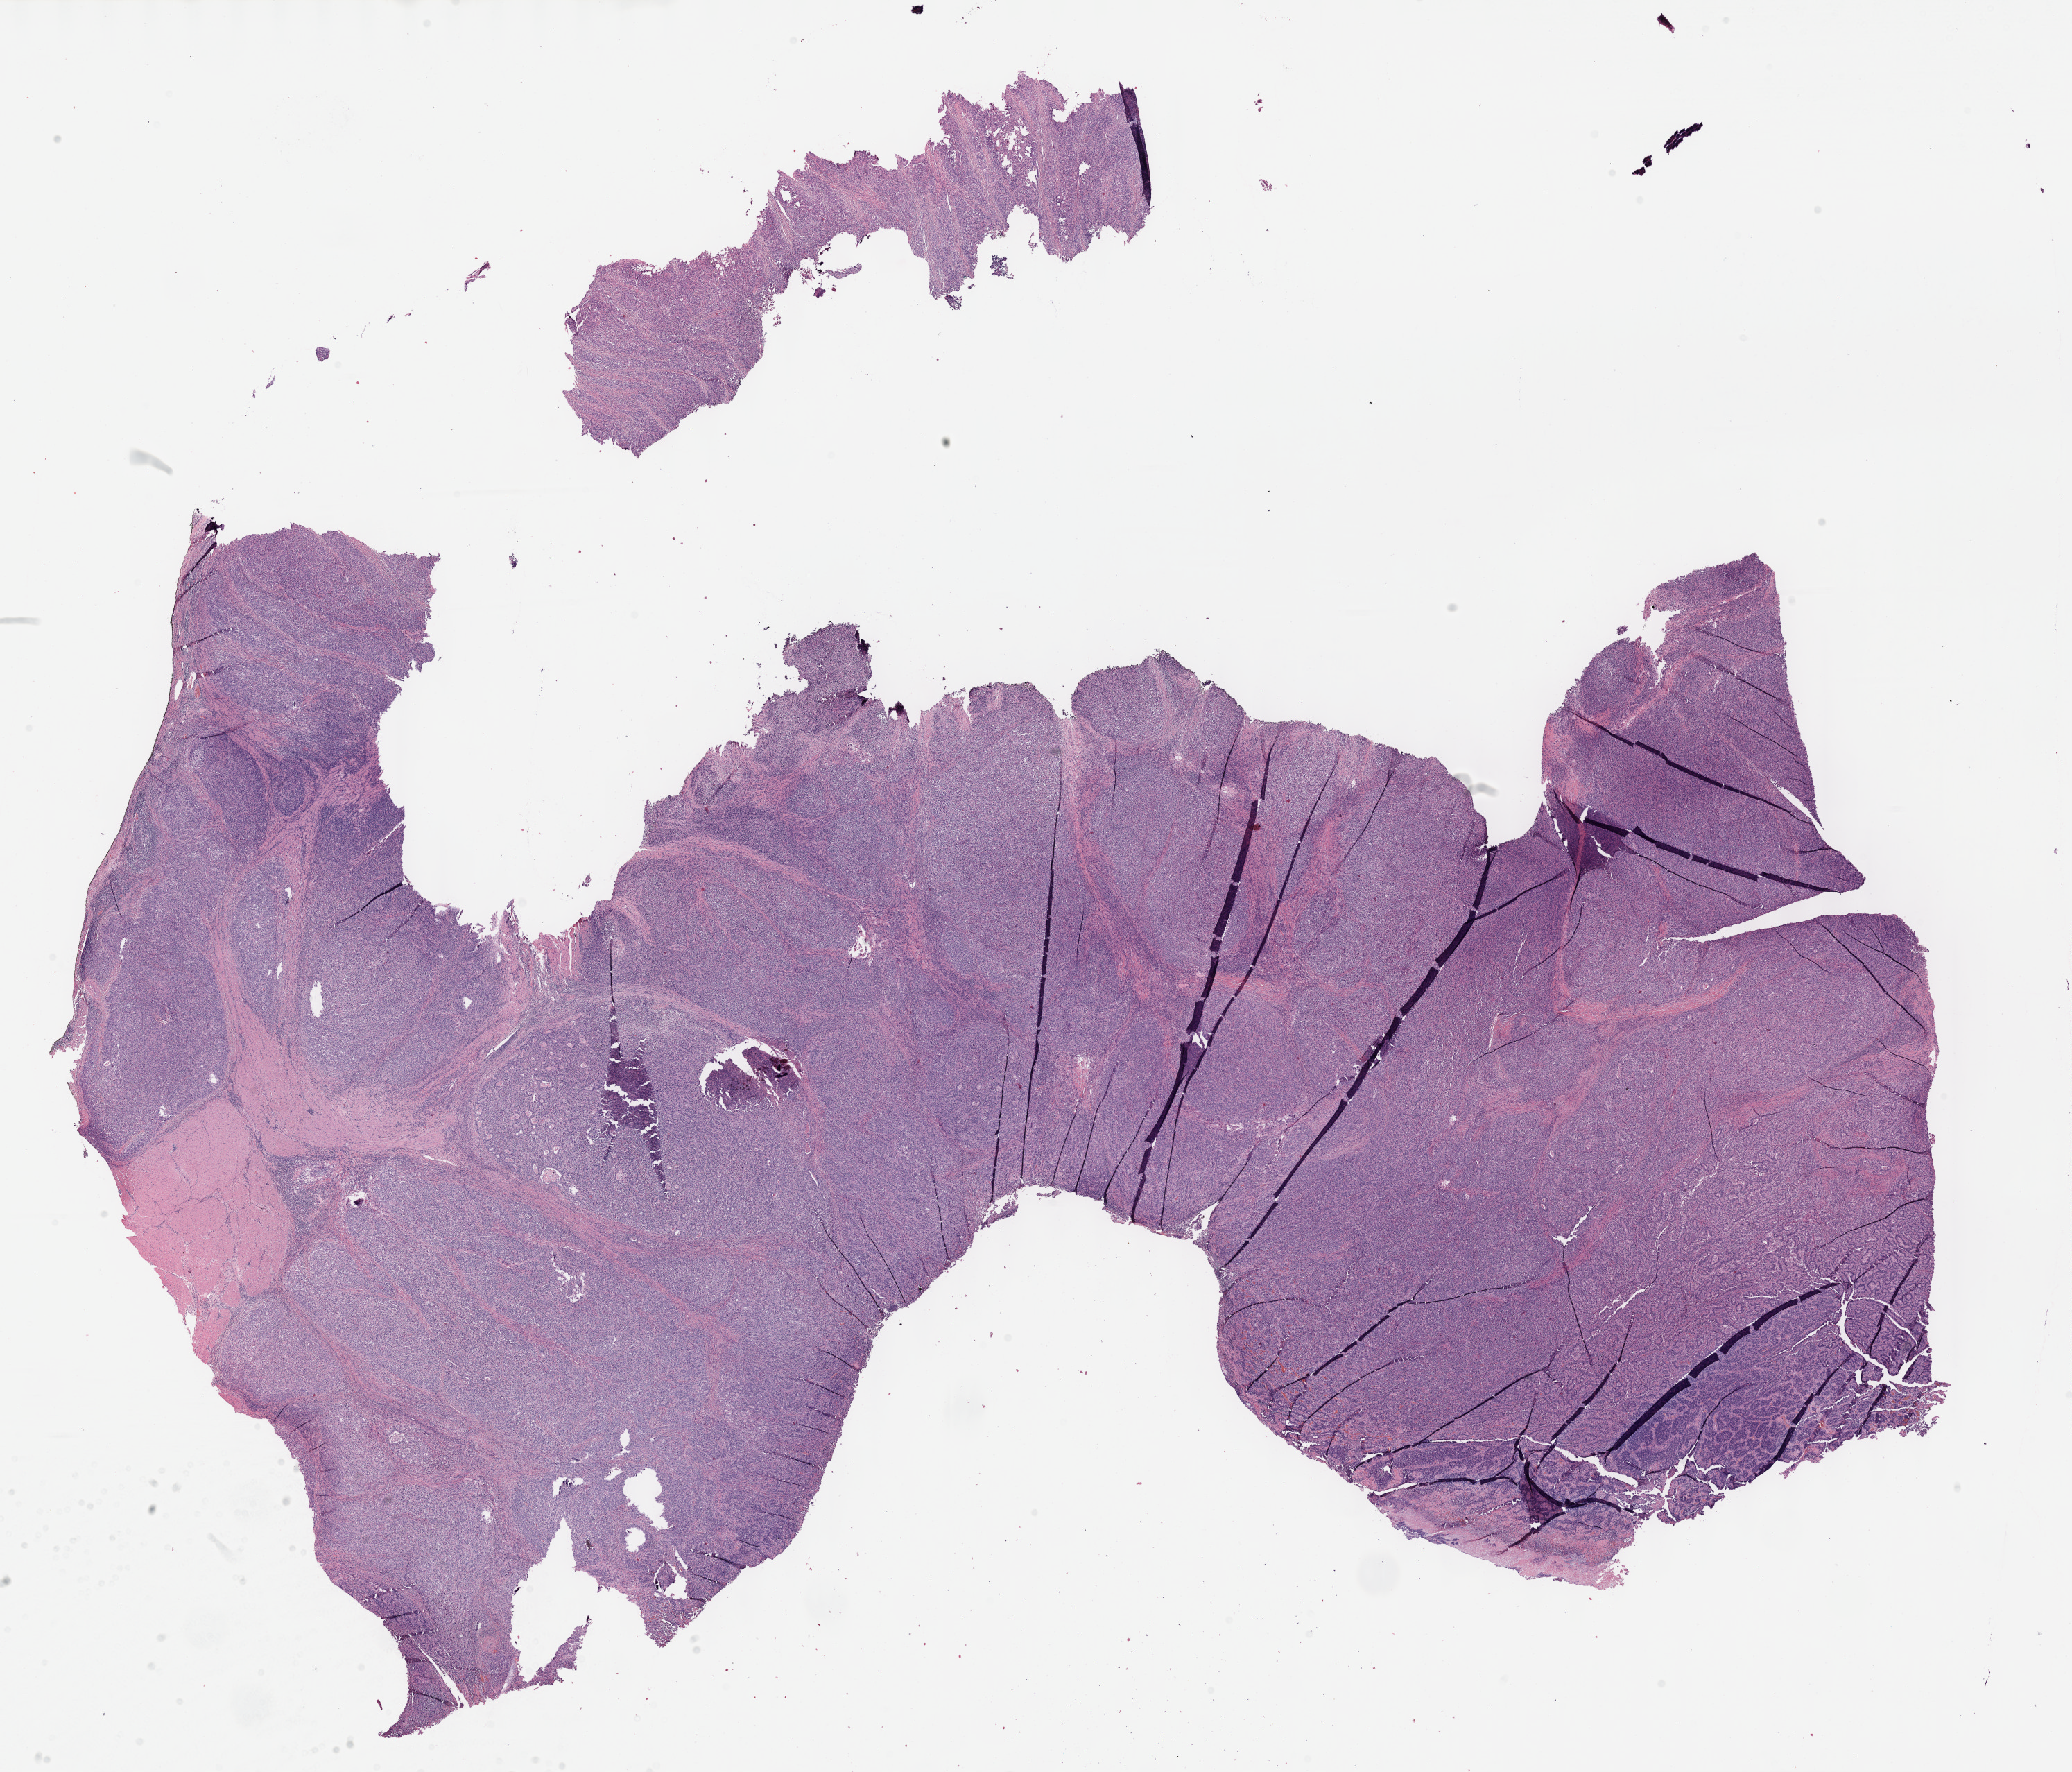
H&E whole-slide image — low-resolution overview of the scanned area, about 24.1 x 20.6 mm, formalin-fixed paraffin-embedded (FFPE) diagnostic section, primary tumour sample from the stomach. Male patient; age at initial diagnosis 76 years. Histologic grade: G3 (poorly differentiated).
Lymph nodes positive (case pathology): 24 of 41 examined. Diagnosis: Tubular adenocarcinoma (body of stomach). AJCC pathologic stage: IIIB (7th edition).